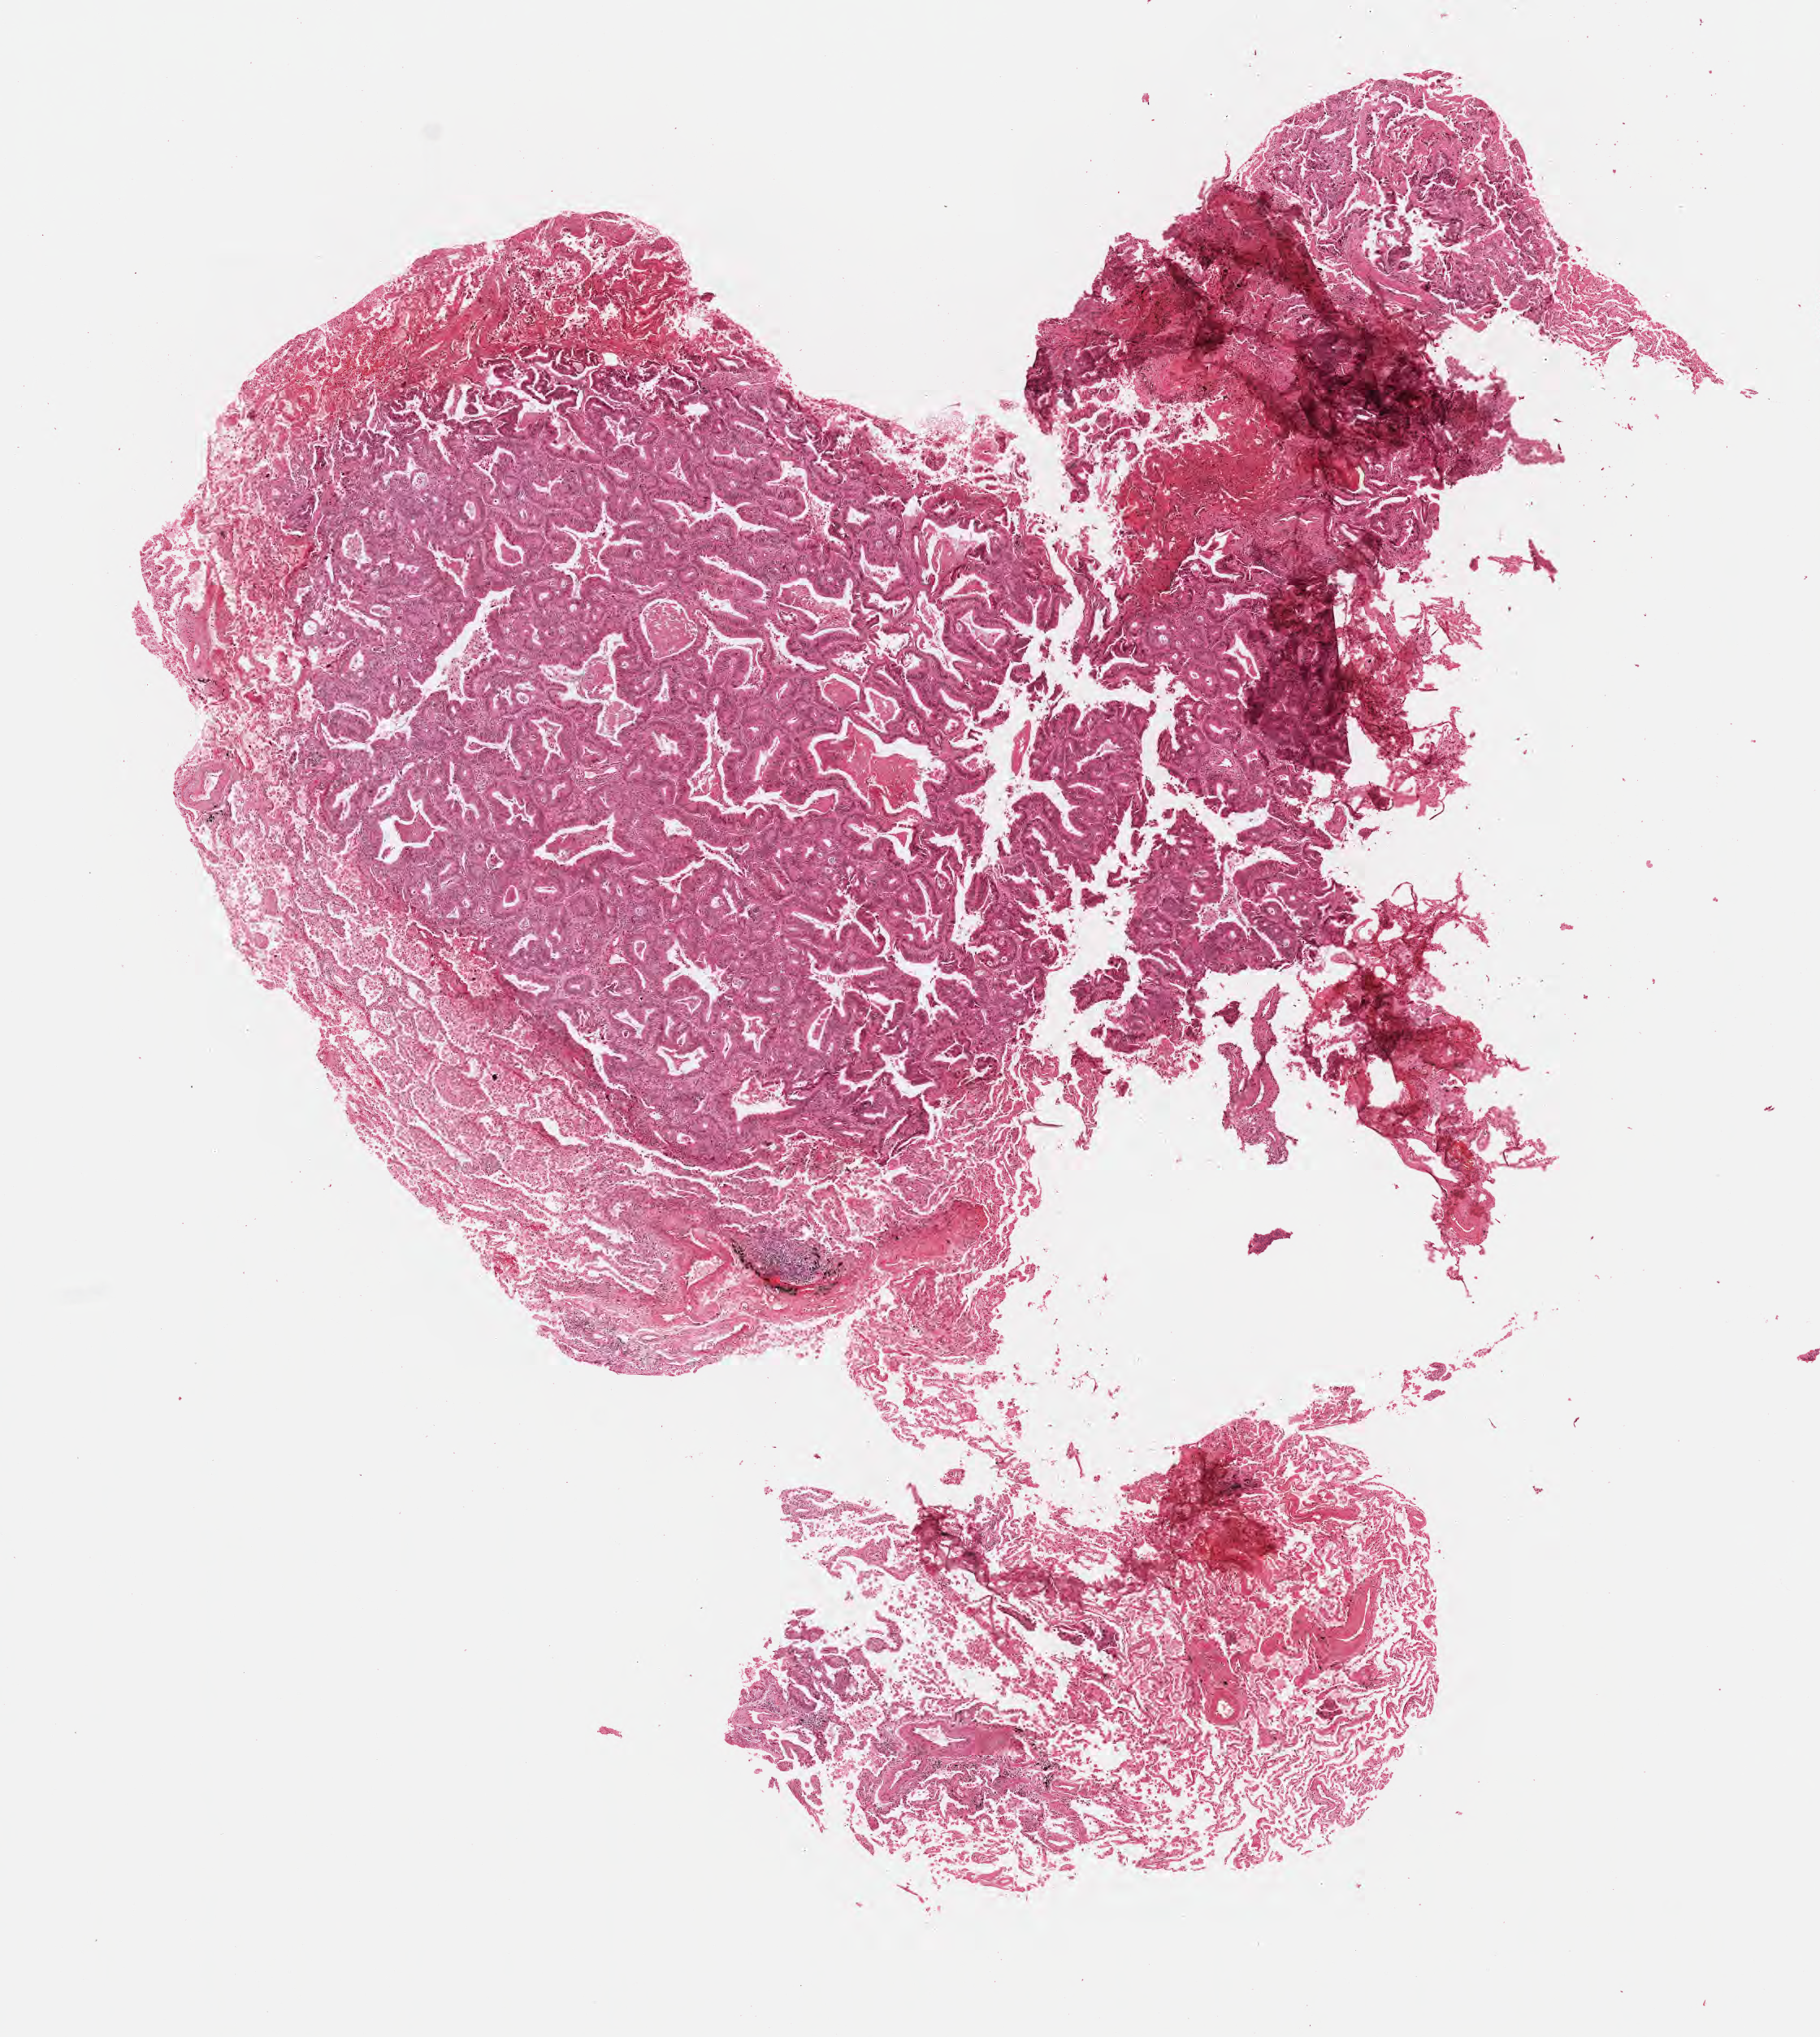
H&E whole-slide image, low-resolution overview of the scanned area, about 9.1 x 10.1 mm. Formalin-fixed paraffin-embedded section. Primary tumor. Anatomic site: upper lobe of right lung. Male patient, 66 years old. Composition of this section per pathologist review: tumor cells 70%, tumor nuclei 70%, stromal cells 23%, necrosis 3%, normal cells 4%. Inflammatory infiltration, as recorded: lymphocyte infiltration 3%, monocyte infiltration 5%, neutrophil infiltration 6%.
* section: top of the tissue portion
* AJCC pathologic stage: Stage IA
* histologic diagnosis: Adenocarcinoma, NOS